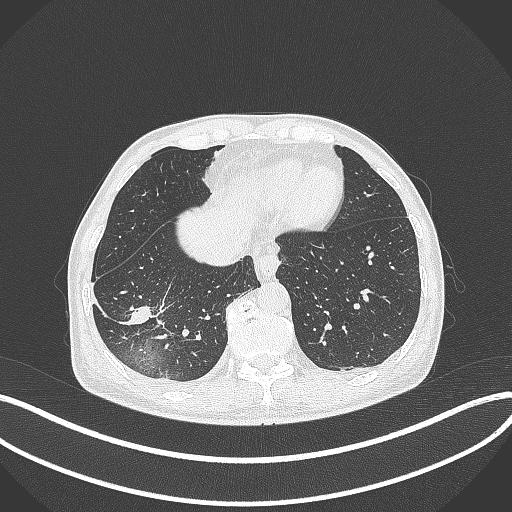
Chest CT, one axial slice; slice 93 of 388 in the series (ordered by position); reconstruction kernel B70f; lung window (W 1500 / L -600 HU); 1 mm slice thickness; 512 × 512 image matrix, field of view 400 × 400 mm. Patient: male, 64 years. Case-level facts recorded for this patient, not image findings: clinical TNM (as recorded): T3 N0 M0.
Annotated regions visible in this slice (rectangle marked by the reading radiologist):
- lung tumour (recorded histology: adenocarcinoma): bounding box <115,300,158,336> (left, top, right, bottom; pixels)